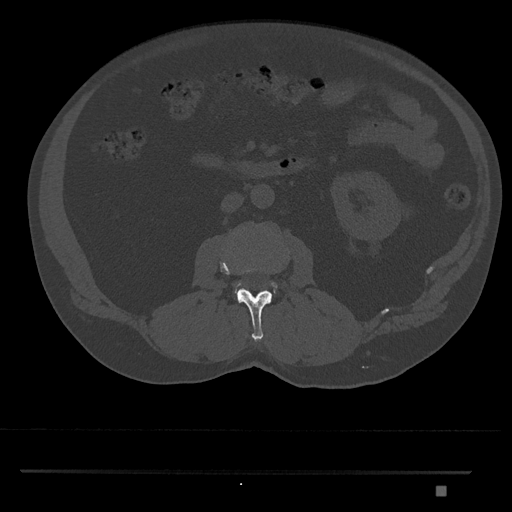
CT including the spine, one axial slice; bone window (W 1800 / L 400 HU); 0.5 mm slice thickness; 512 × 512 image matrix, field of view 429 × 429 mm. Patient: male, 65 years. Case-level facts recorded for this patient, not image findings: primary cancer: prostate.
Annotated regions visible in this slice (semi-automatic segmentation, software-assisted and operator-edited):
- L2 vertebra: box from (x=220, y=259) to (x=272, y=342) px
- L3 vertebra: (x=235, y=282)–(x=277, y=293)